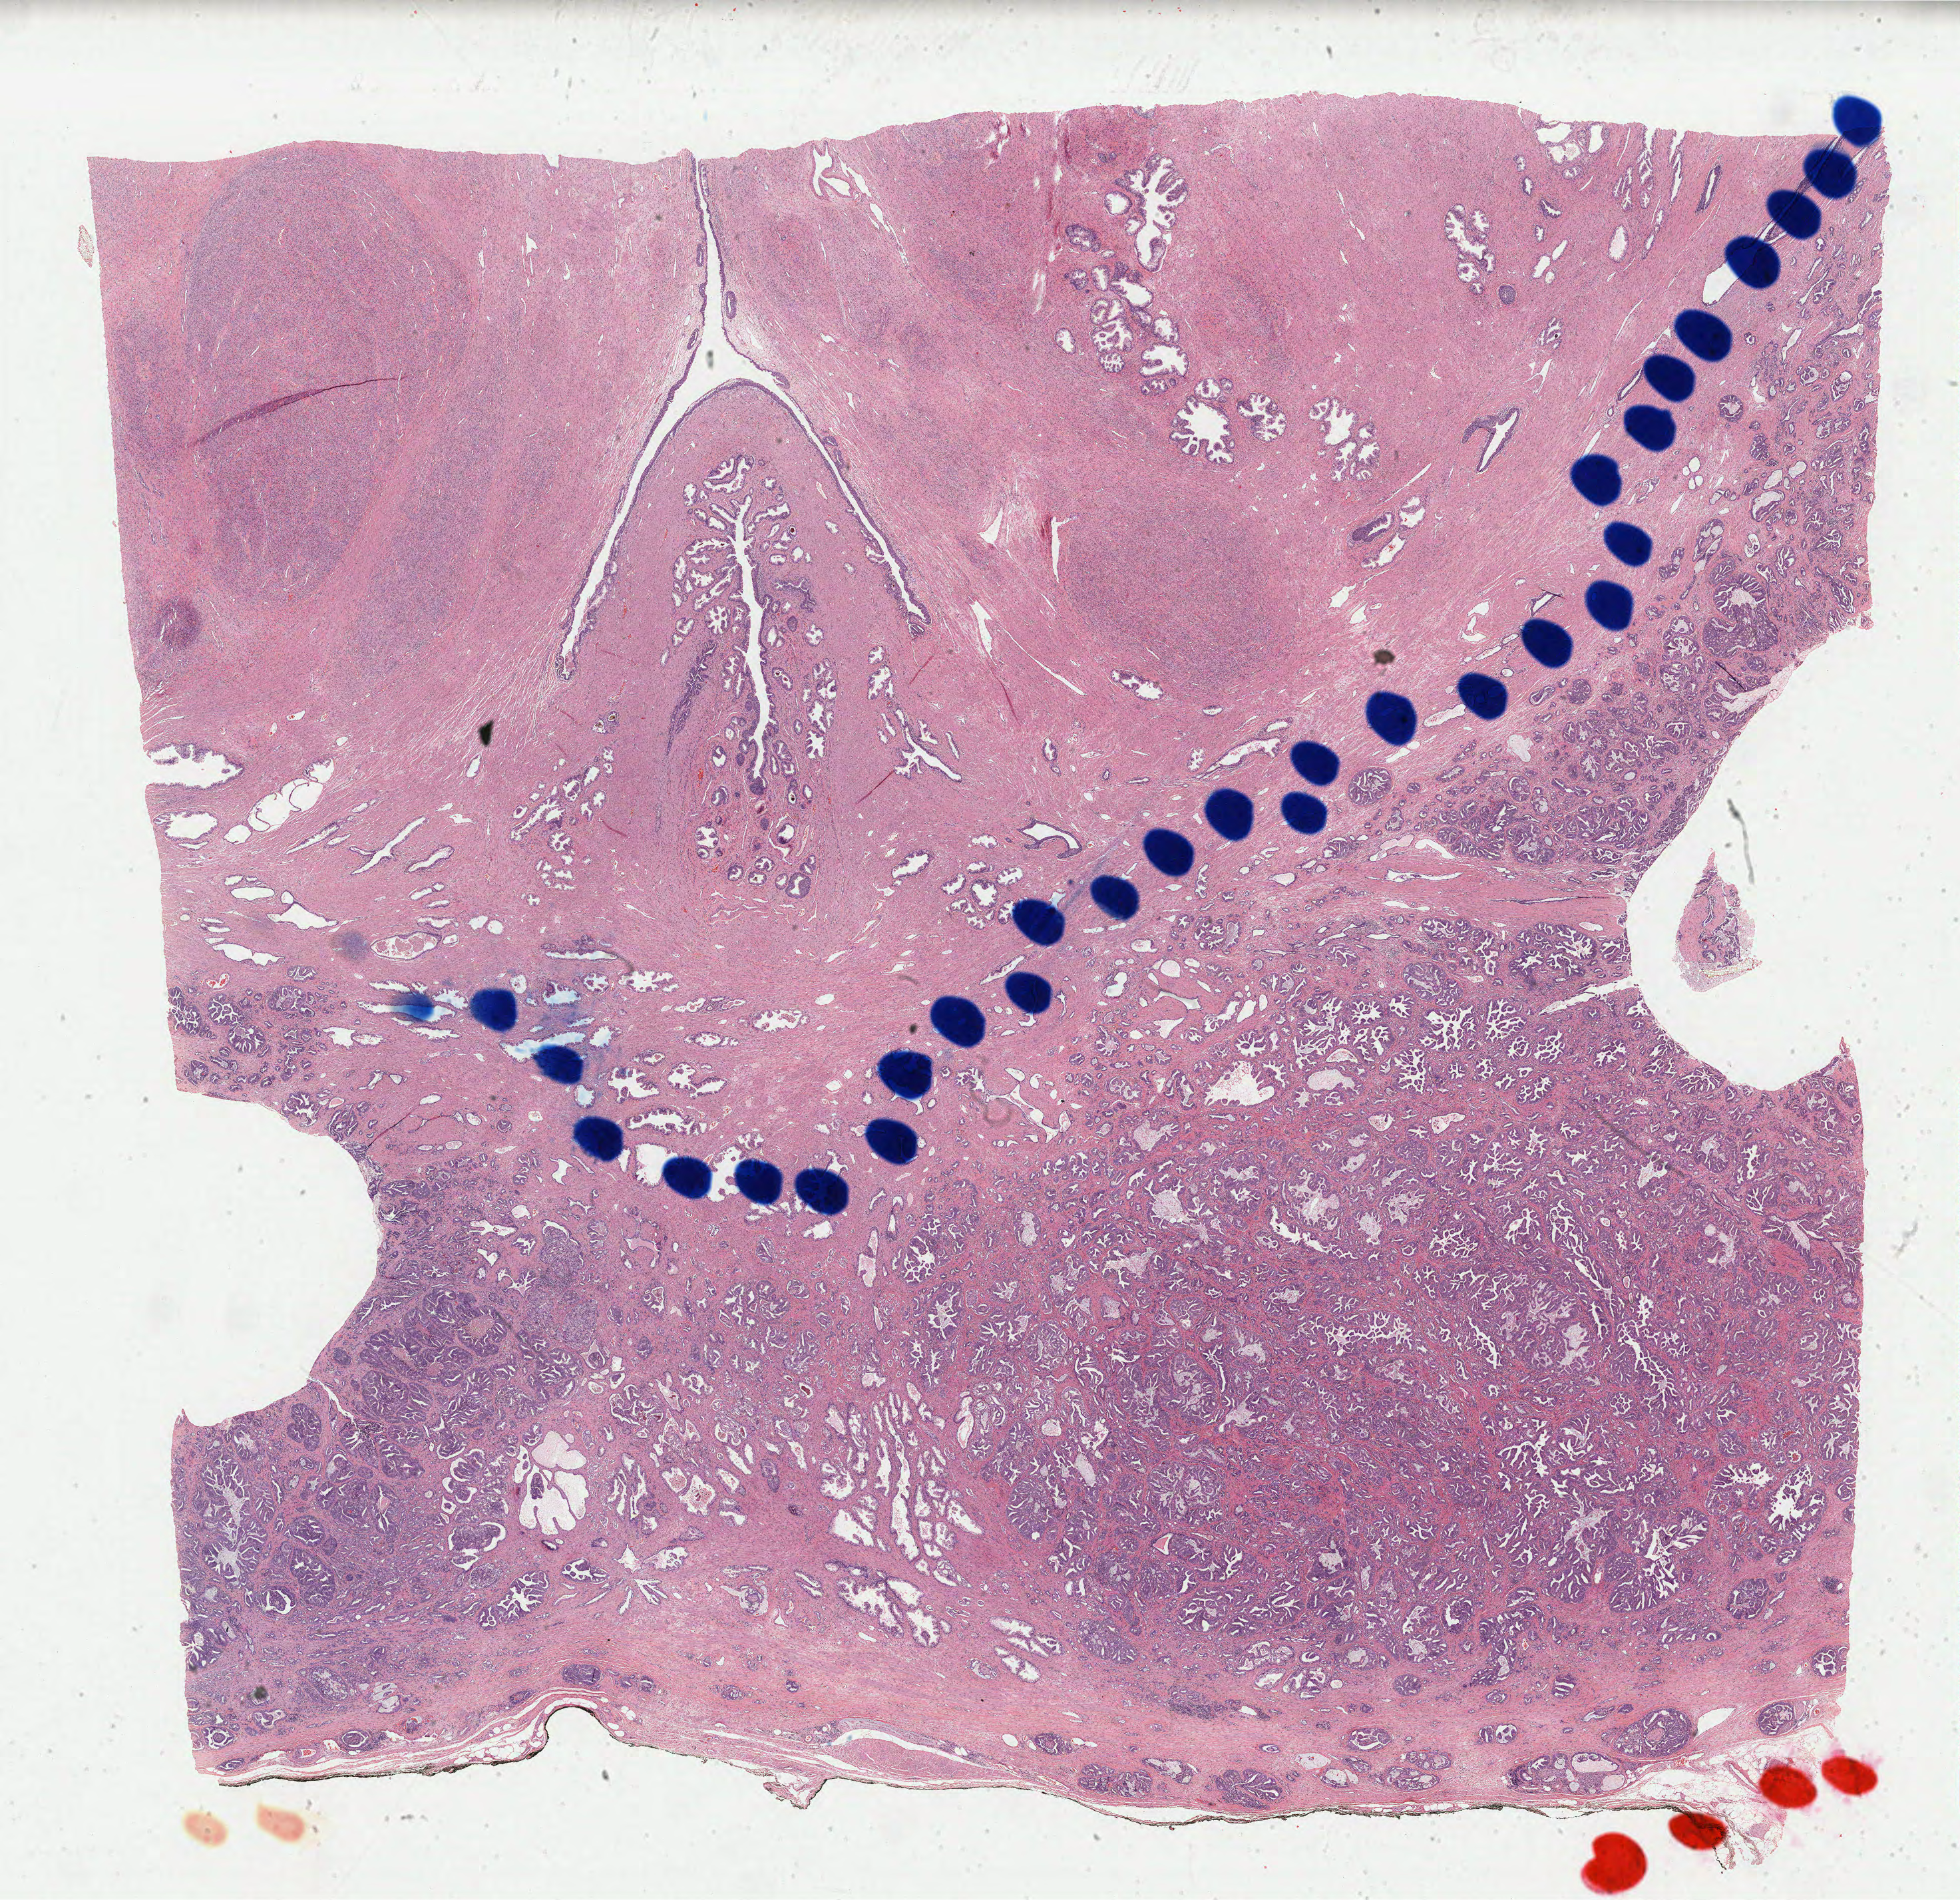
Whole-slide histology image, Hematoxylin and eosin (H&E) stained, a low-resolution overview of the entire scanned area, about 23.4 x 22.7 mm (acquisition: 40x scan); formalin-fixed paraffin-embedded (FFPE) diagnostic section; sample: primary tumour, prostate. Male patient; age at initial diagnosis 61 years. Gleason score: 9 (4+5).
• pathologic diagnosis: Infiltrating duct carcinoma, NOS (prostate gland)